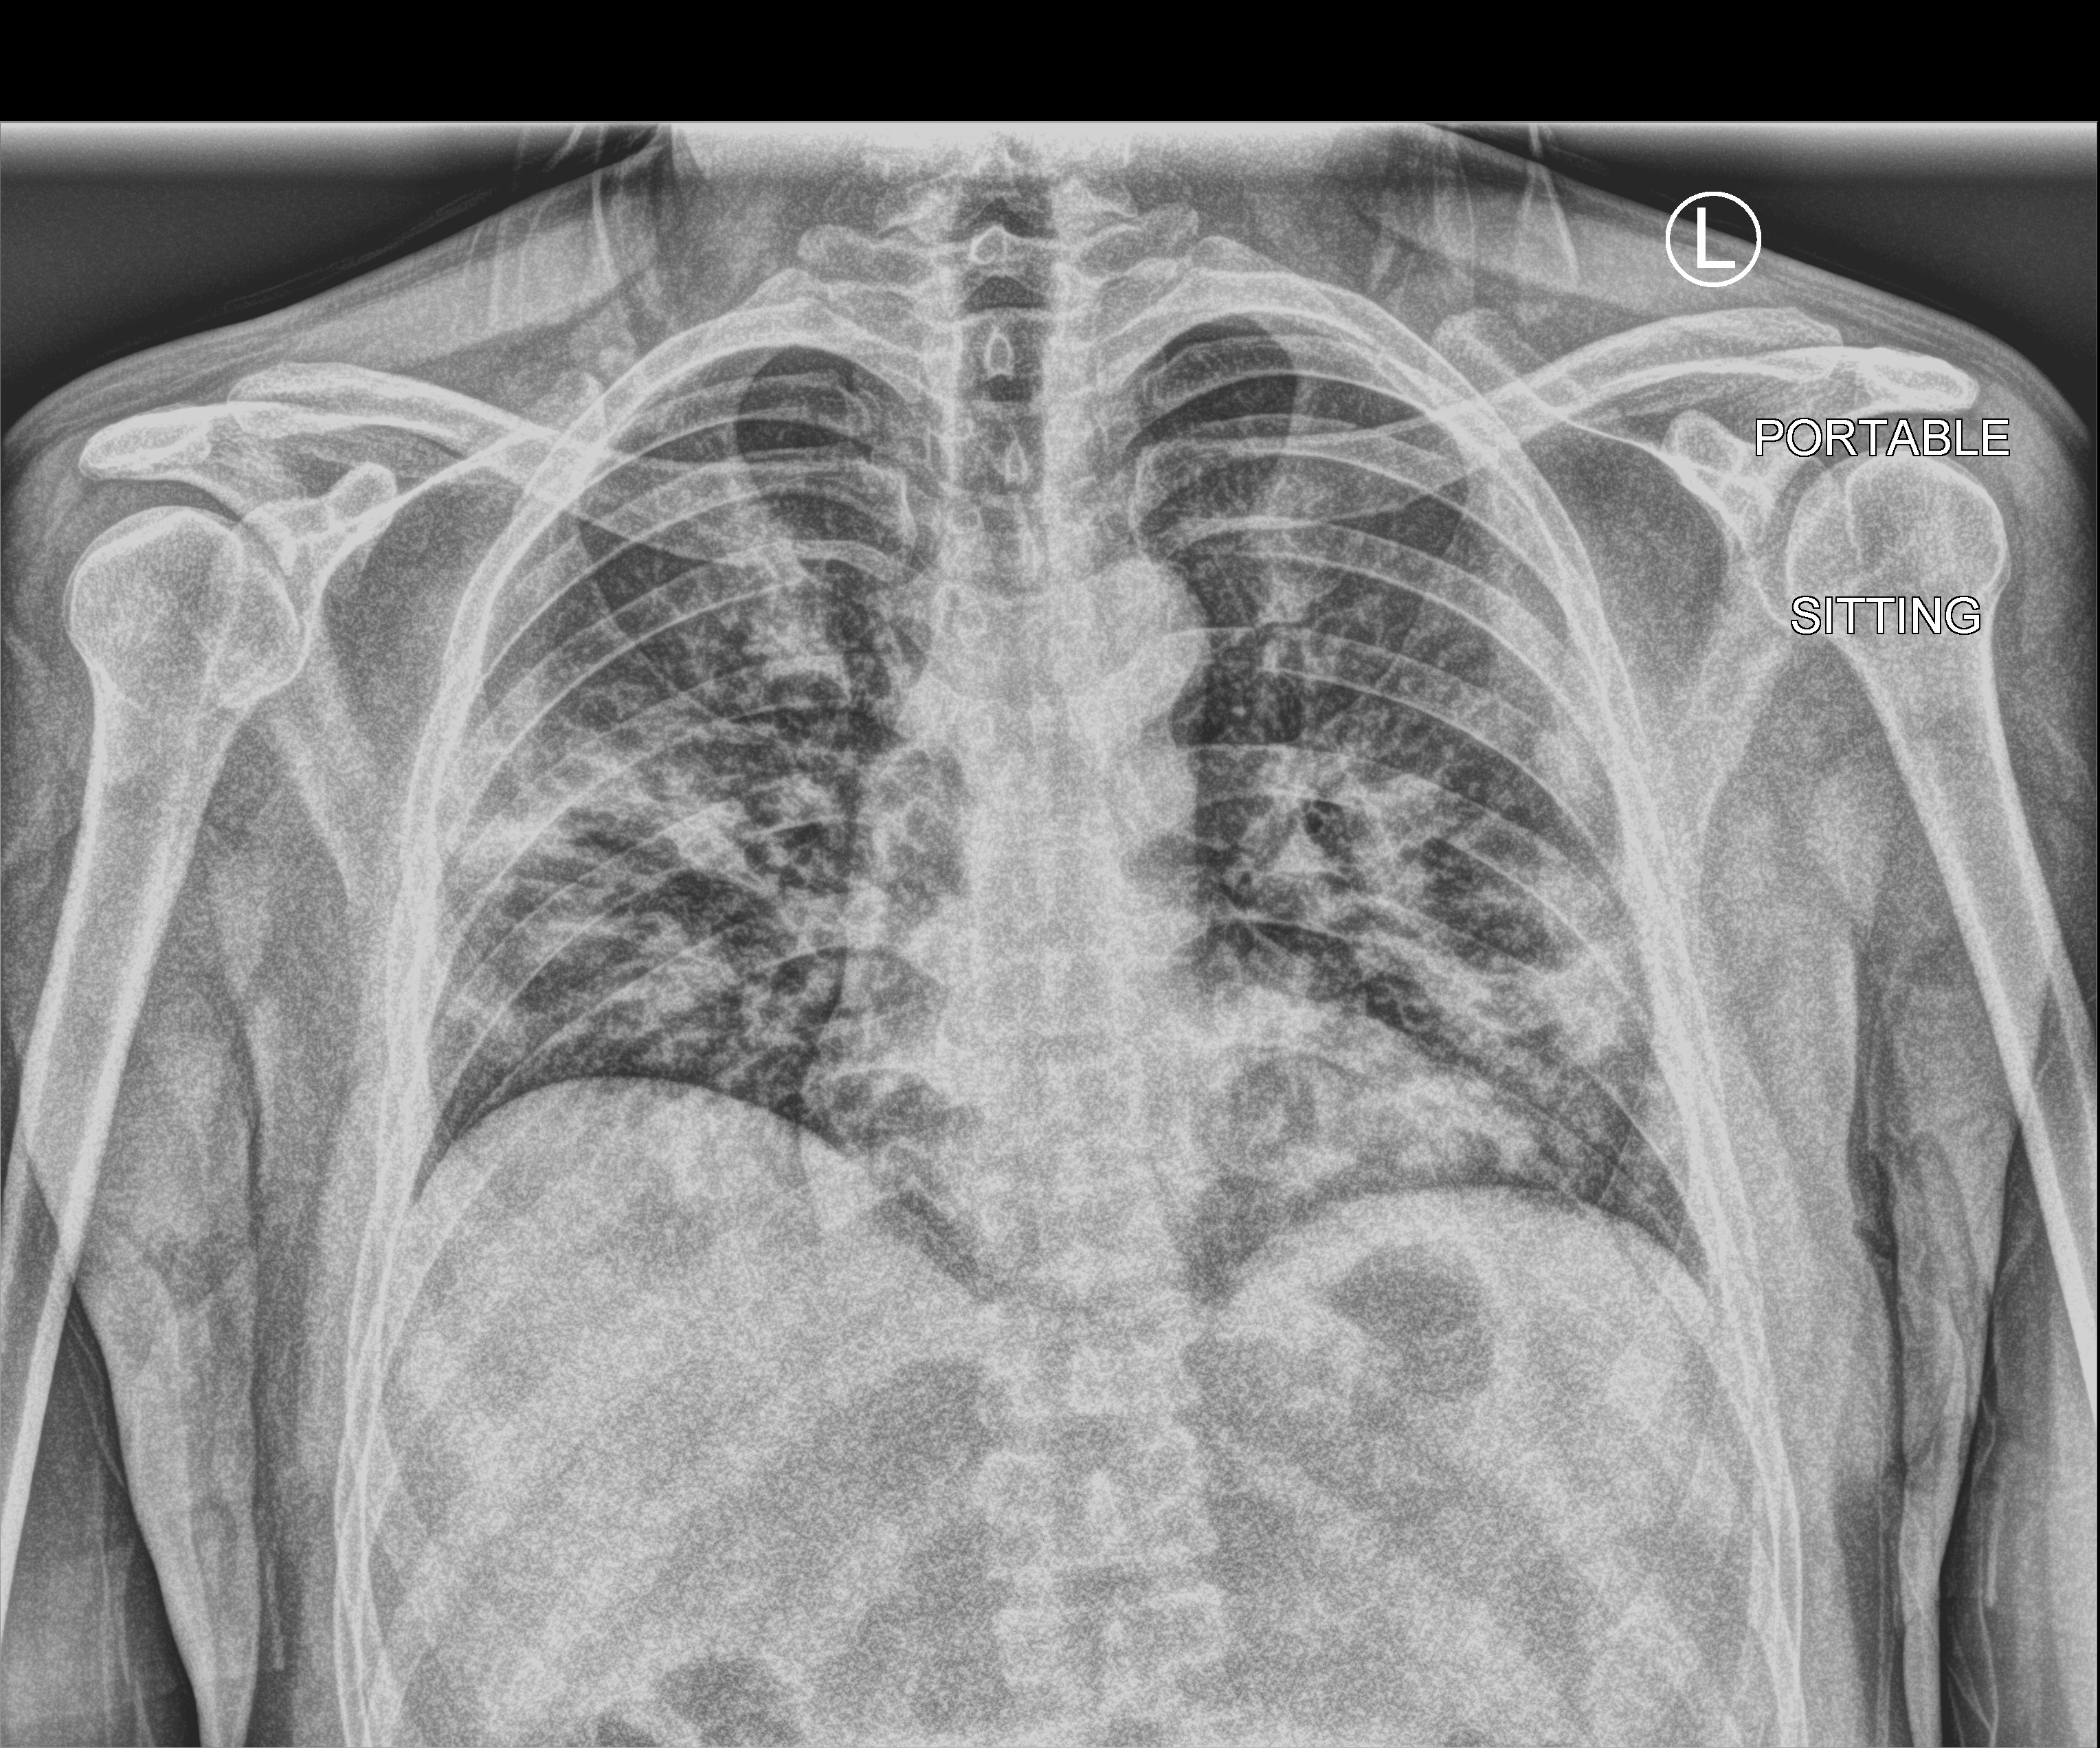
Bedside chest radiograph (computed radiography); anteroposterior (AP) projection. Patient hospitalised with COVID-19; male, aged 18–59 years.
From the hospital-stay record, not from the radiograph (when in the stay this image was taken is not recorded):
- diabetes (admission record): no